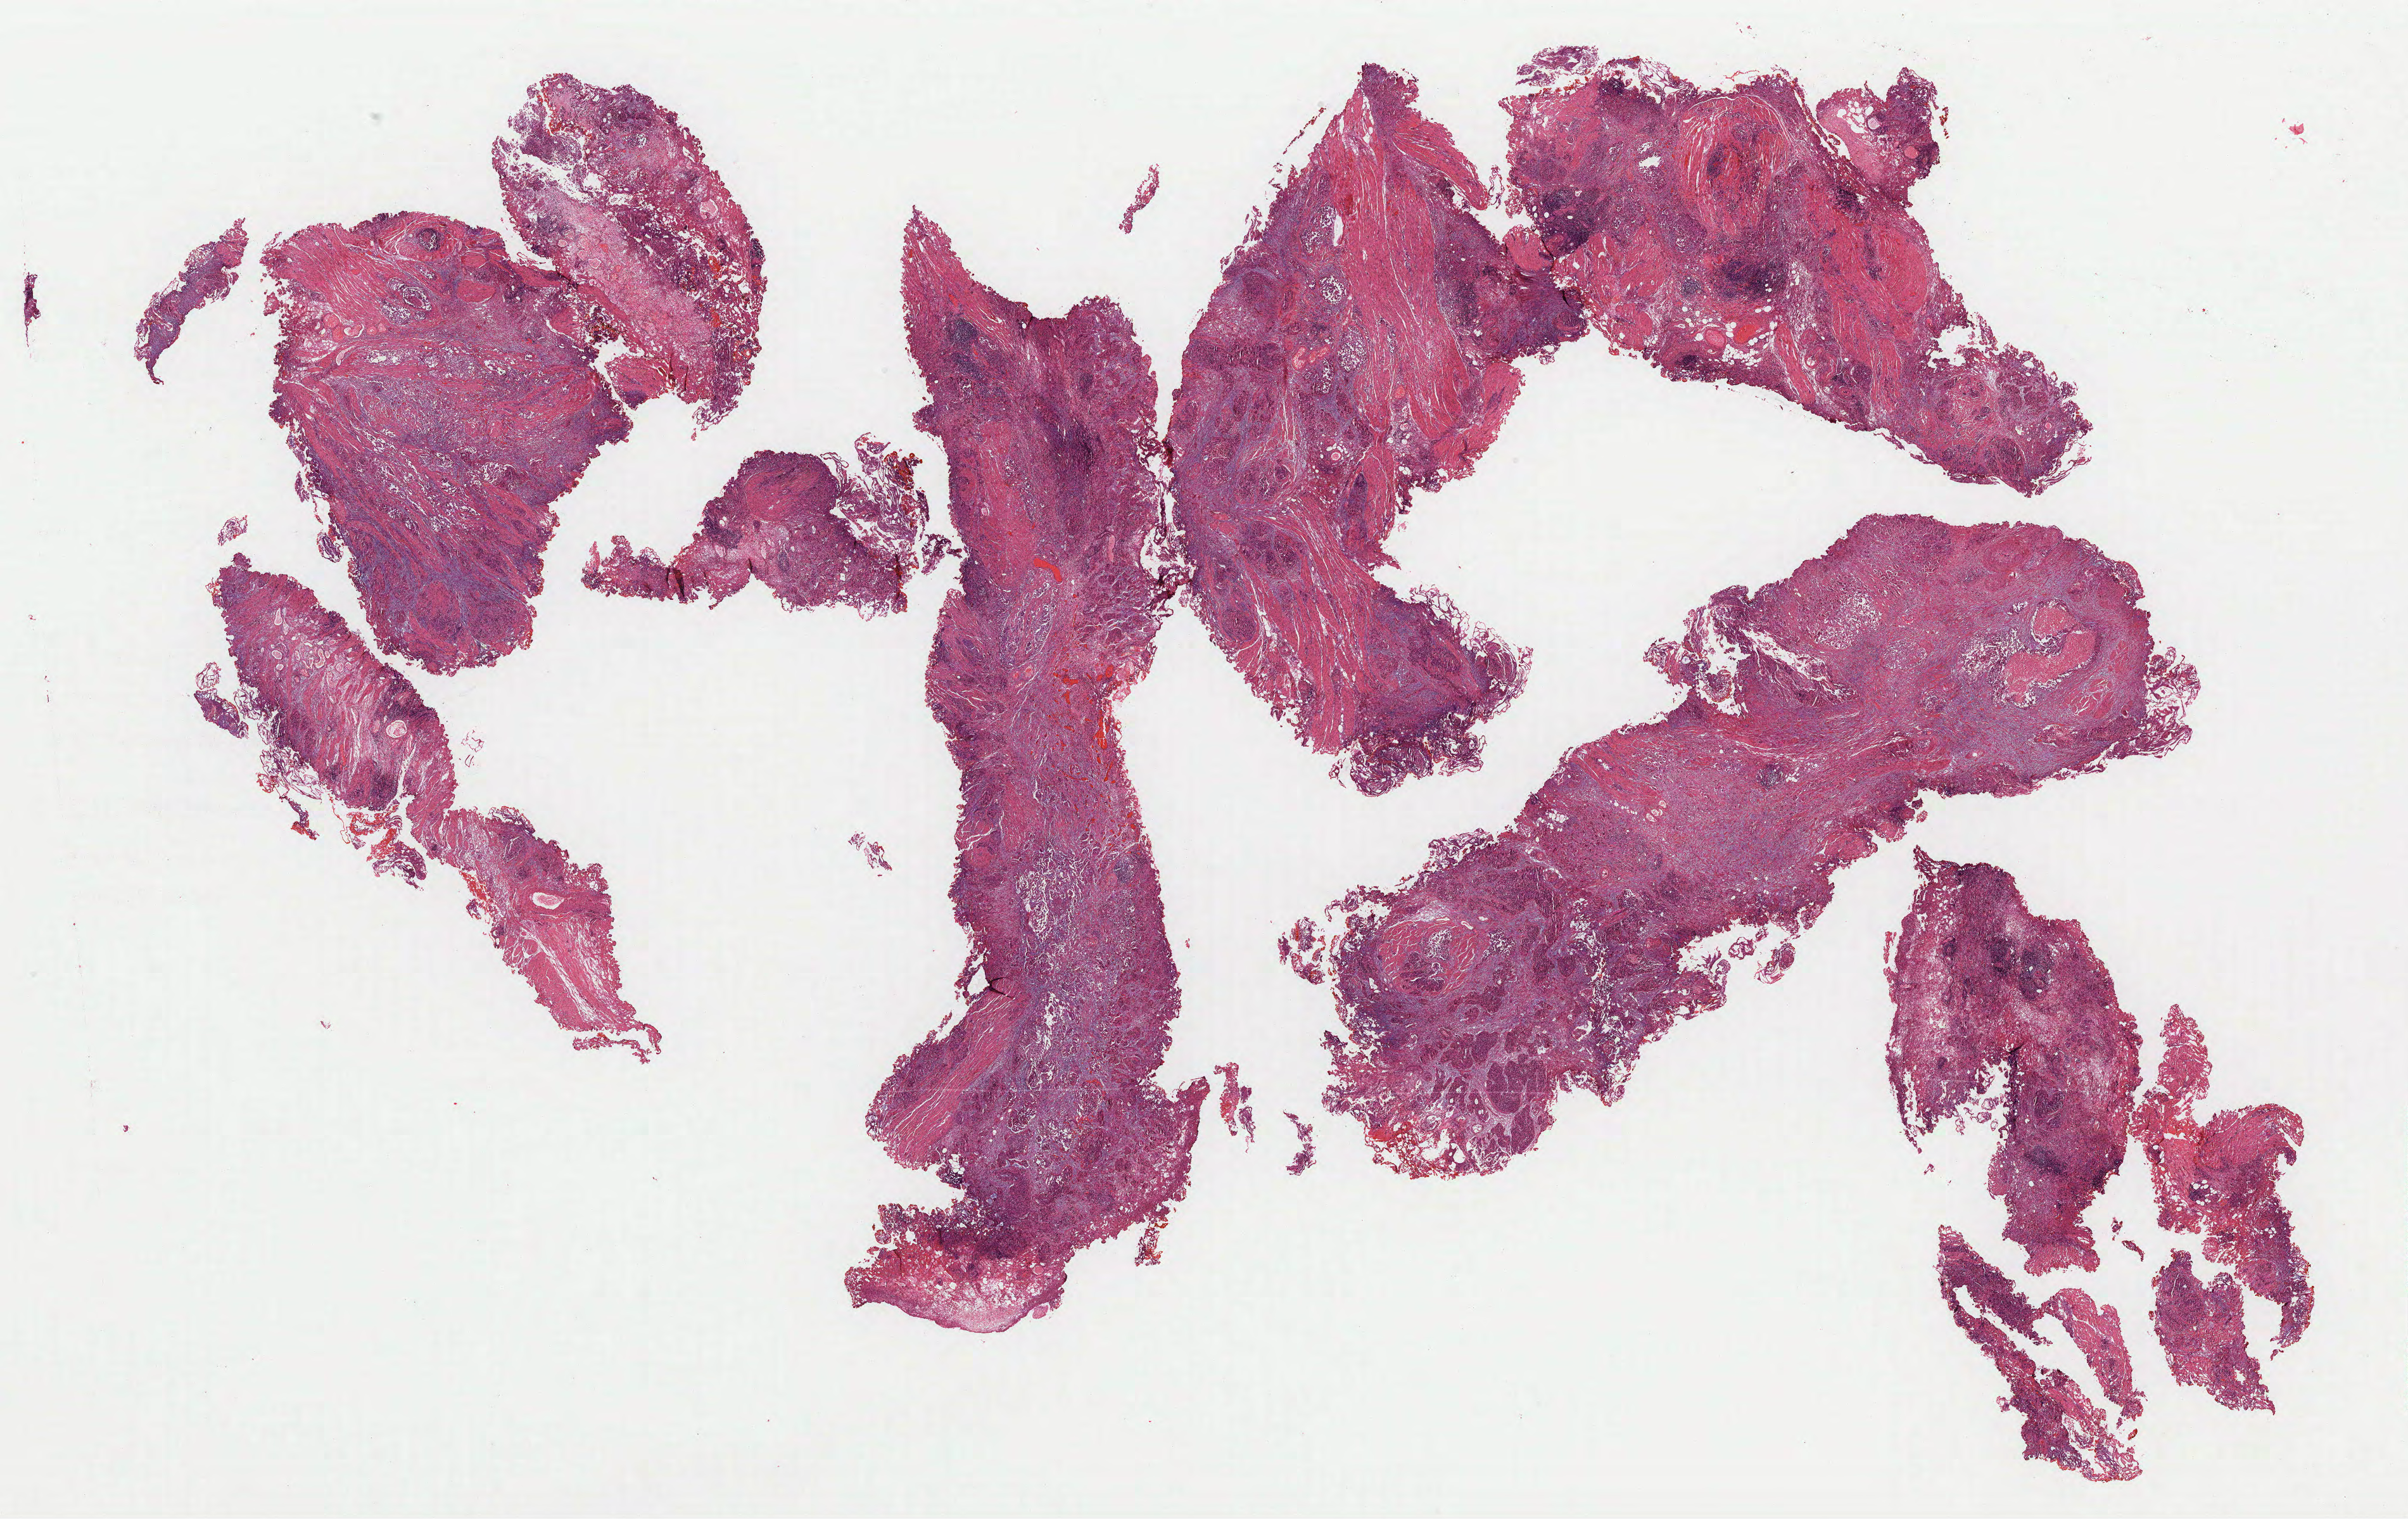
H&E whole-slide image, whole scanned area (about 30.2 x 19.0 mm, slide scanned at 40x) shown as a low-resolution overview, formalin-fixed paraffin-embedded (FFPE) diagnostic section, sample: primary tumour, bladder. Patient: male, age at initial diagnosis 74 years.
Histologic diagnosis: Transitional cell carcinoma.